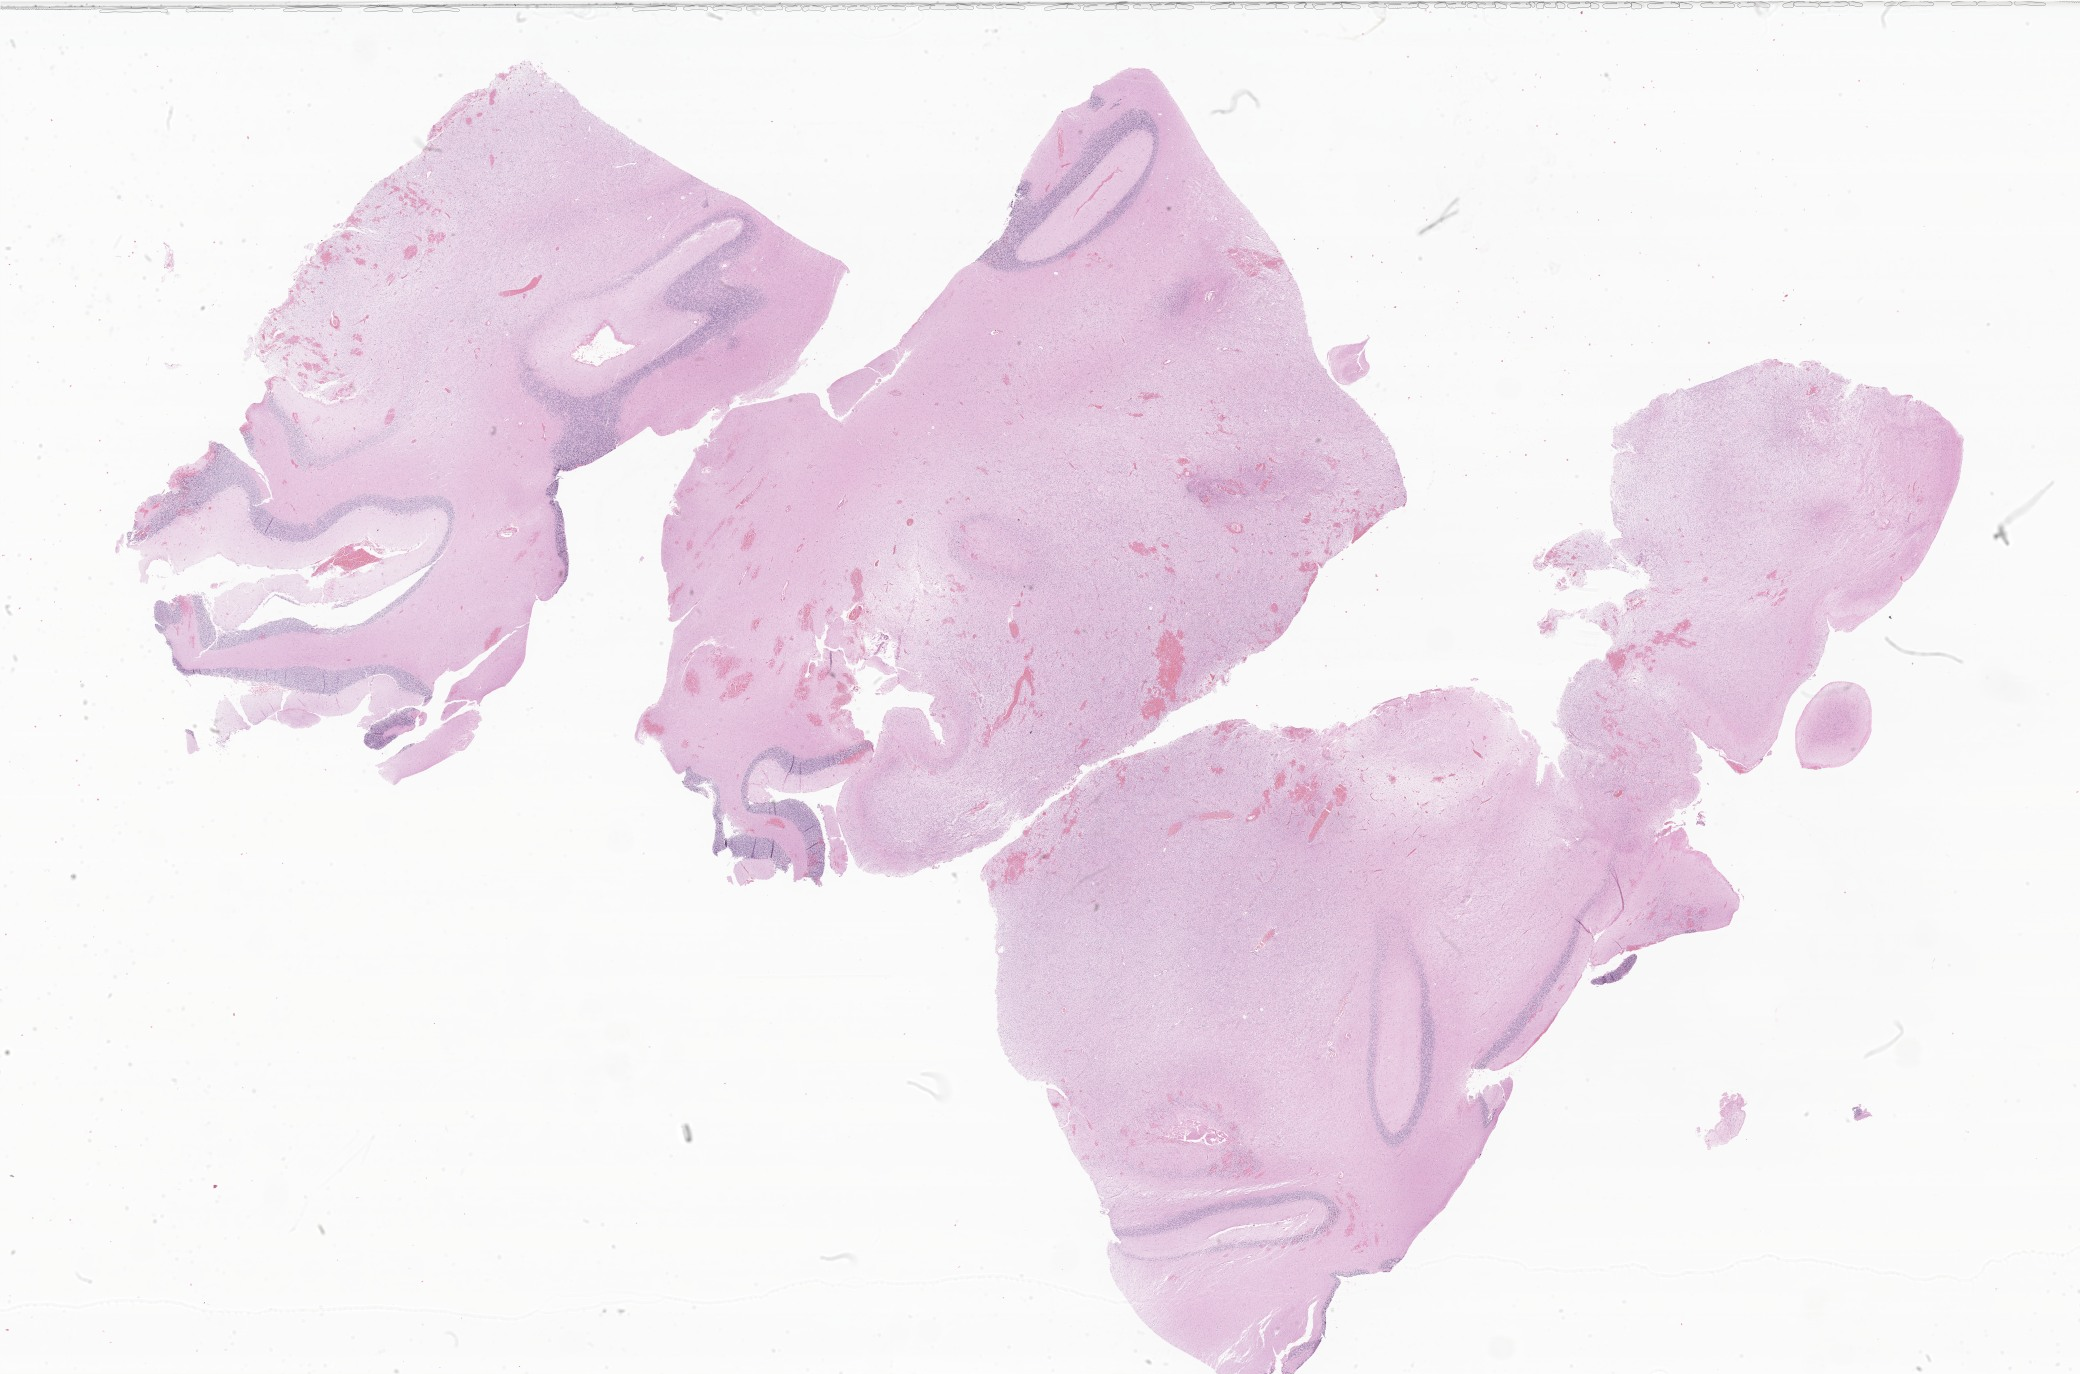
Whole-slide image, hematoxylin and eosin (H&E) stain of tumor tissue from the cerebellum, whole scanned area (about 35.1 x 23.2 mm) shown as a low-resolution overview; FFPE section. Patient male; age 175 months (14 years 7 months).
Diagnosis: Glioma, malignant.